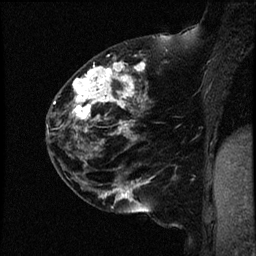
Breast MRI (dynamic contrast-enhanced), one sagittal slice. Position 26 of 44 along the scan axis. Dynamic contrast-enhanced study with each time point stored as its own series, time point 2 of 4 at this slice position (early post-contrast, ordered by acquisition time). 1.5 T. TE 4.2 ms, TR 17.7 ms. 2 mm slice thickness. 256 × 256 image matrix, field of view 200 × 200 mm. Female patient, age 52 years. From the clinical record (not read from this slice): setting: breast cancer imaged before/during neoadjuvant chemotherapy; receptor status: HR-positive, HER2-negative.
Annotated regions visible in this slice (semi-automatically segmented with operator editing):
- analysis volume of interest (the breast-tissue region the enhancement analysis was run in; not a lesion): bounding box (x1, y1, x2, y2) in pixels: (47, 48, 163, 147)
- tumour enhancement mask (voxels above the 100 % enhancement threshold inside the analysis volume of interest): (59, 58, 147, 147)